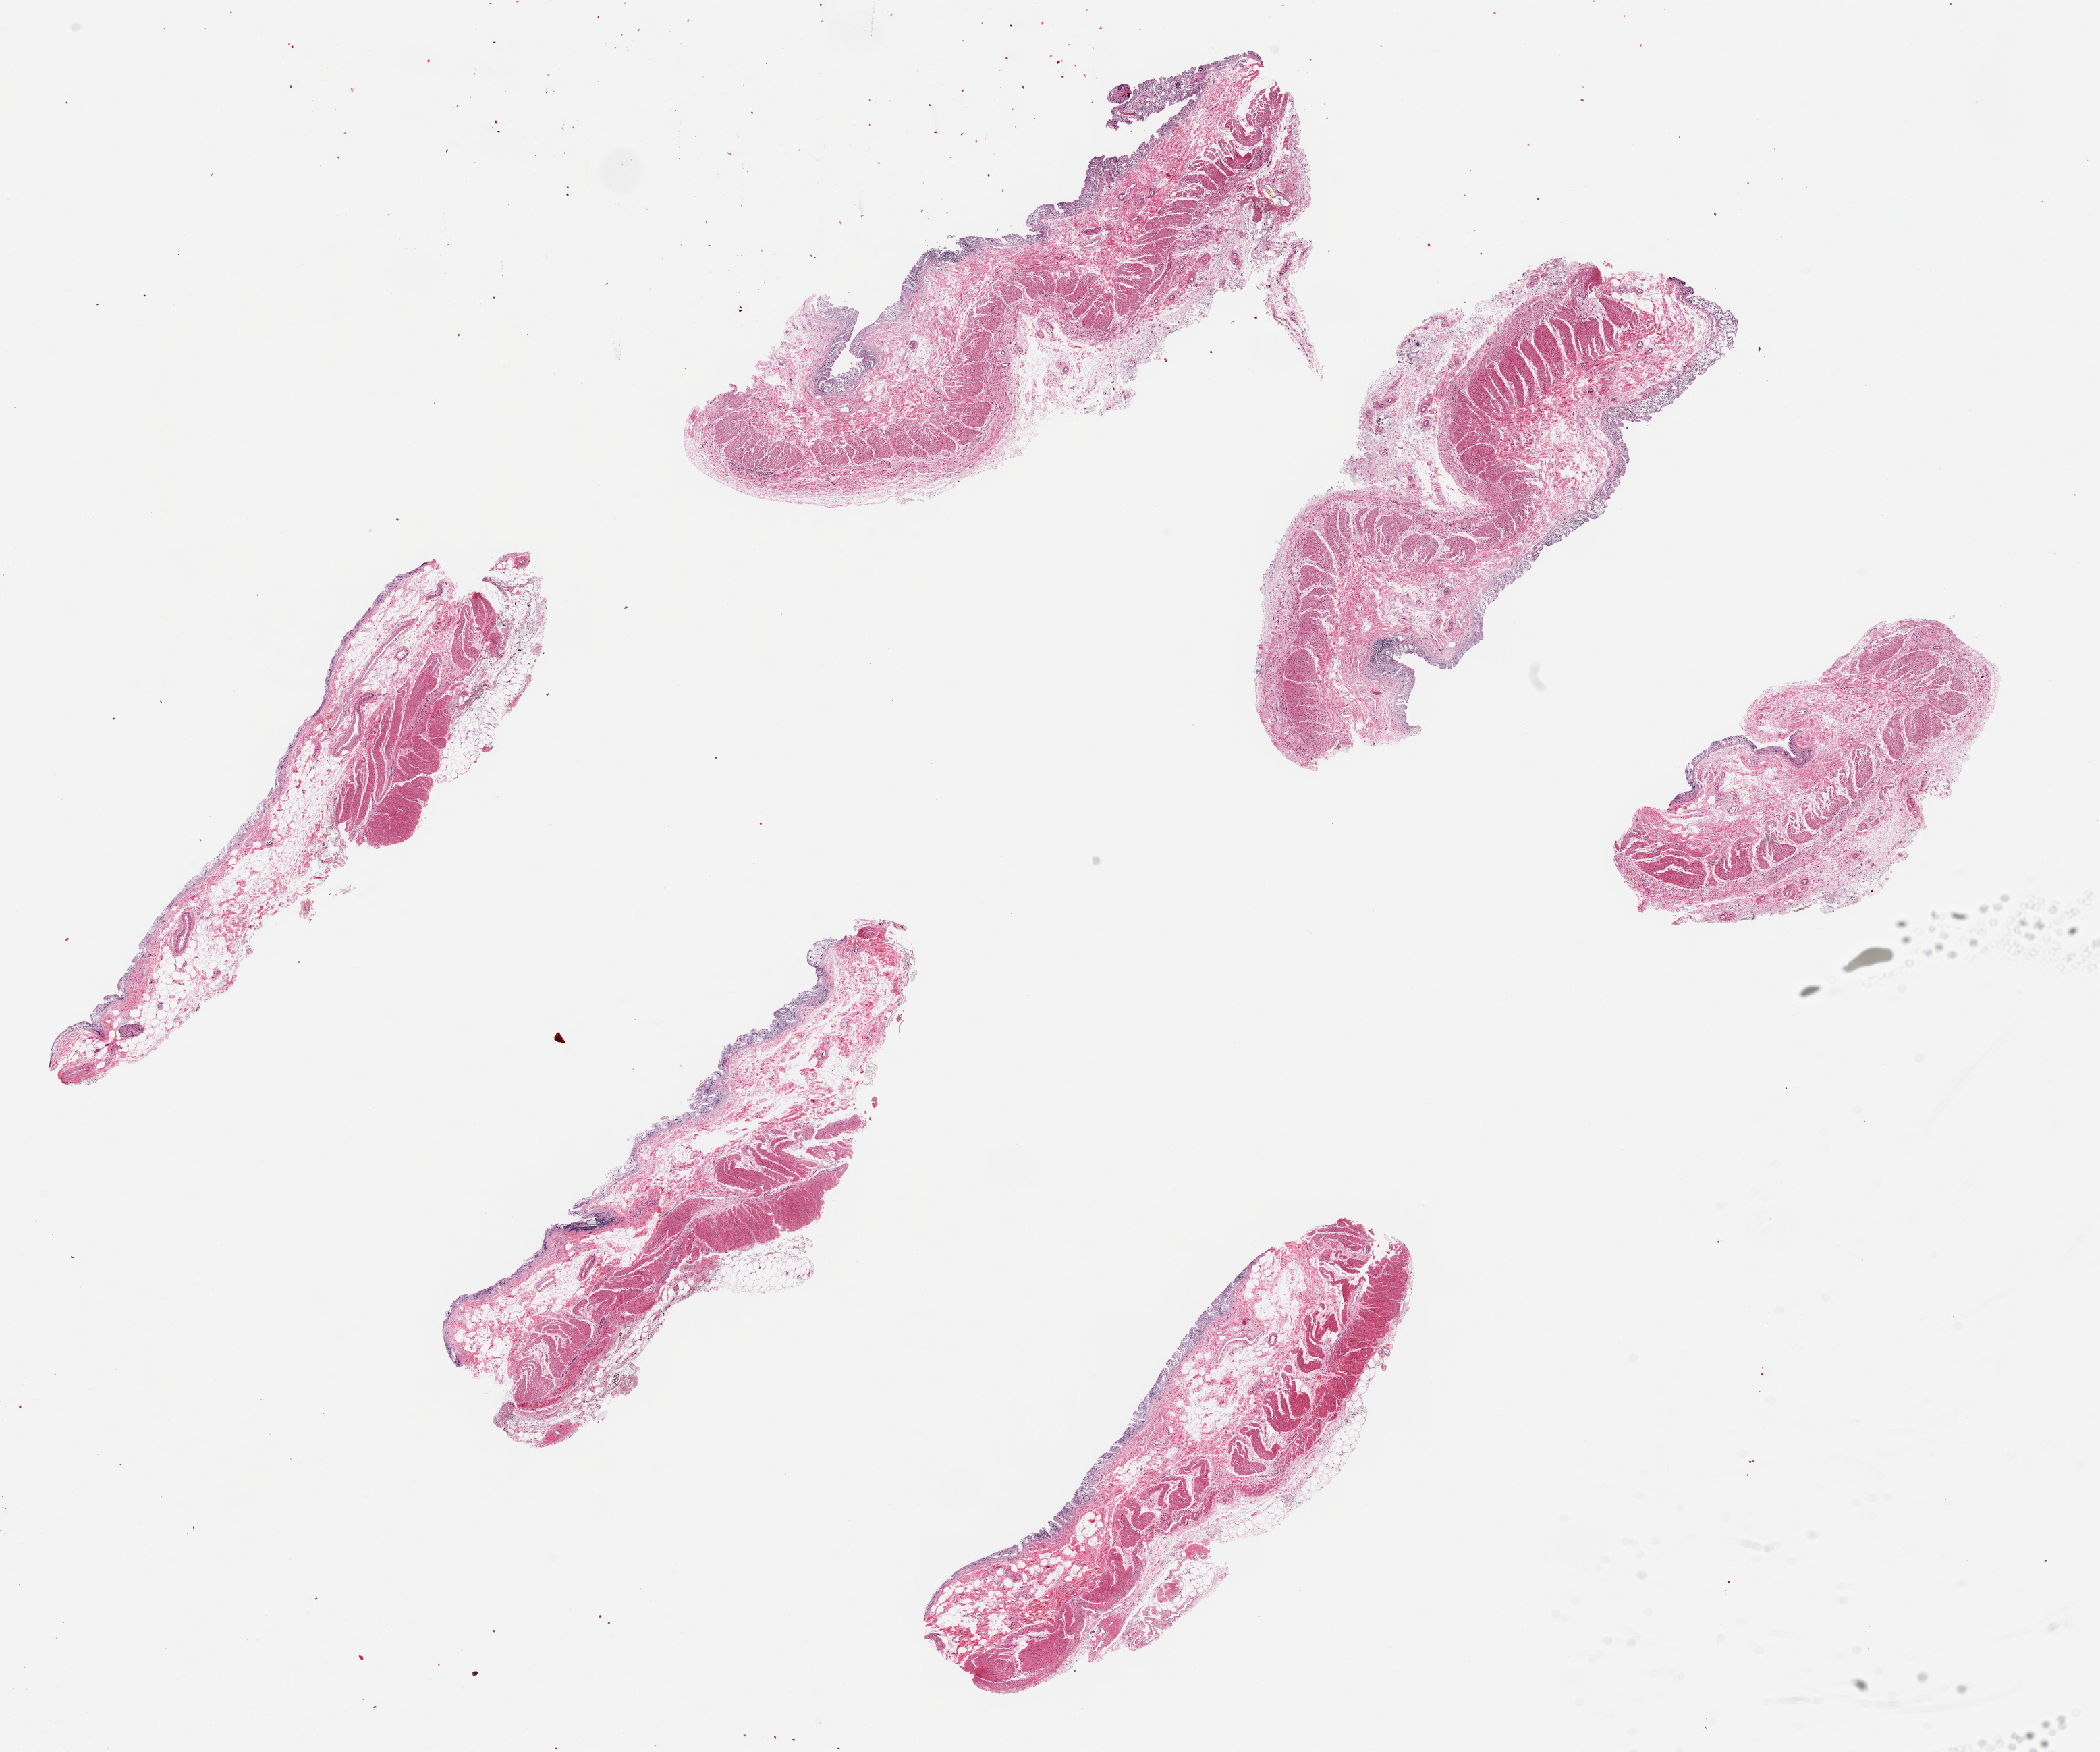
Digitized hematoxylin and eosin (H&E)-stained section, brightfield — shown as a low-resolution overview of the whole scanned area (about 24.6 x 20.5 mm). PAXgene-fixed, paraffin-embedded tissue. Sampled site (target tissue): transverse colon. Donor tissue sample. Donor sex: male.
* pathologist's review note for this sample: 6 pieces, ~7x2.5mm, mucosa totally autolyzed and largely sloughed